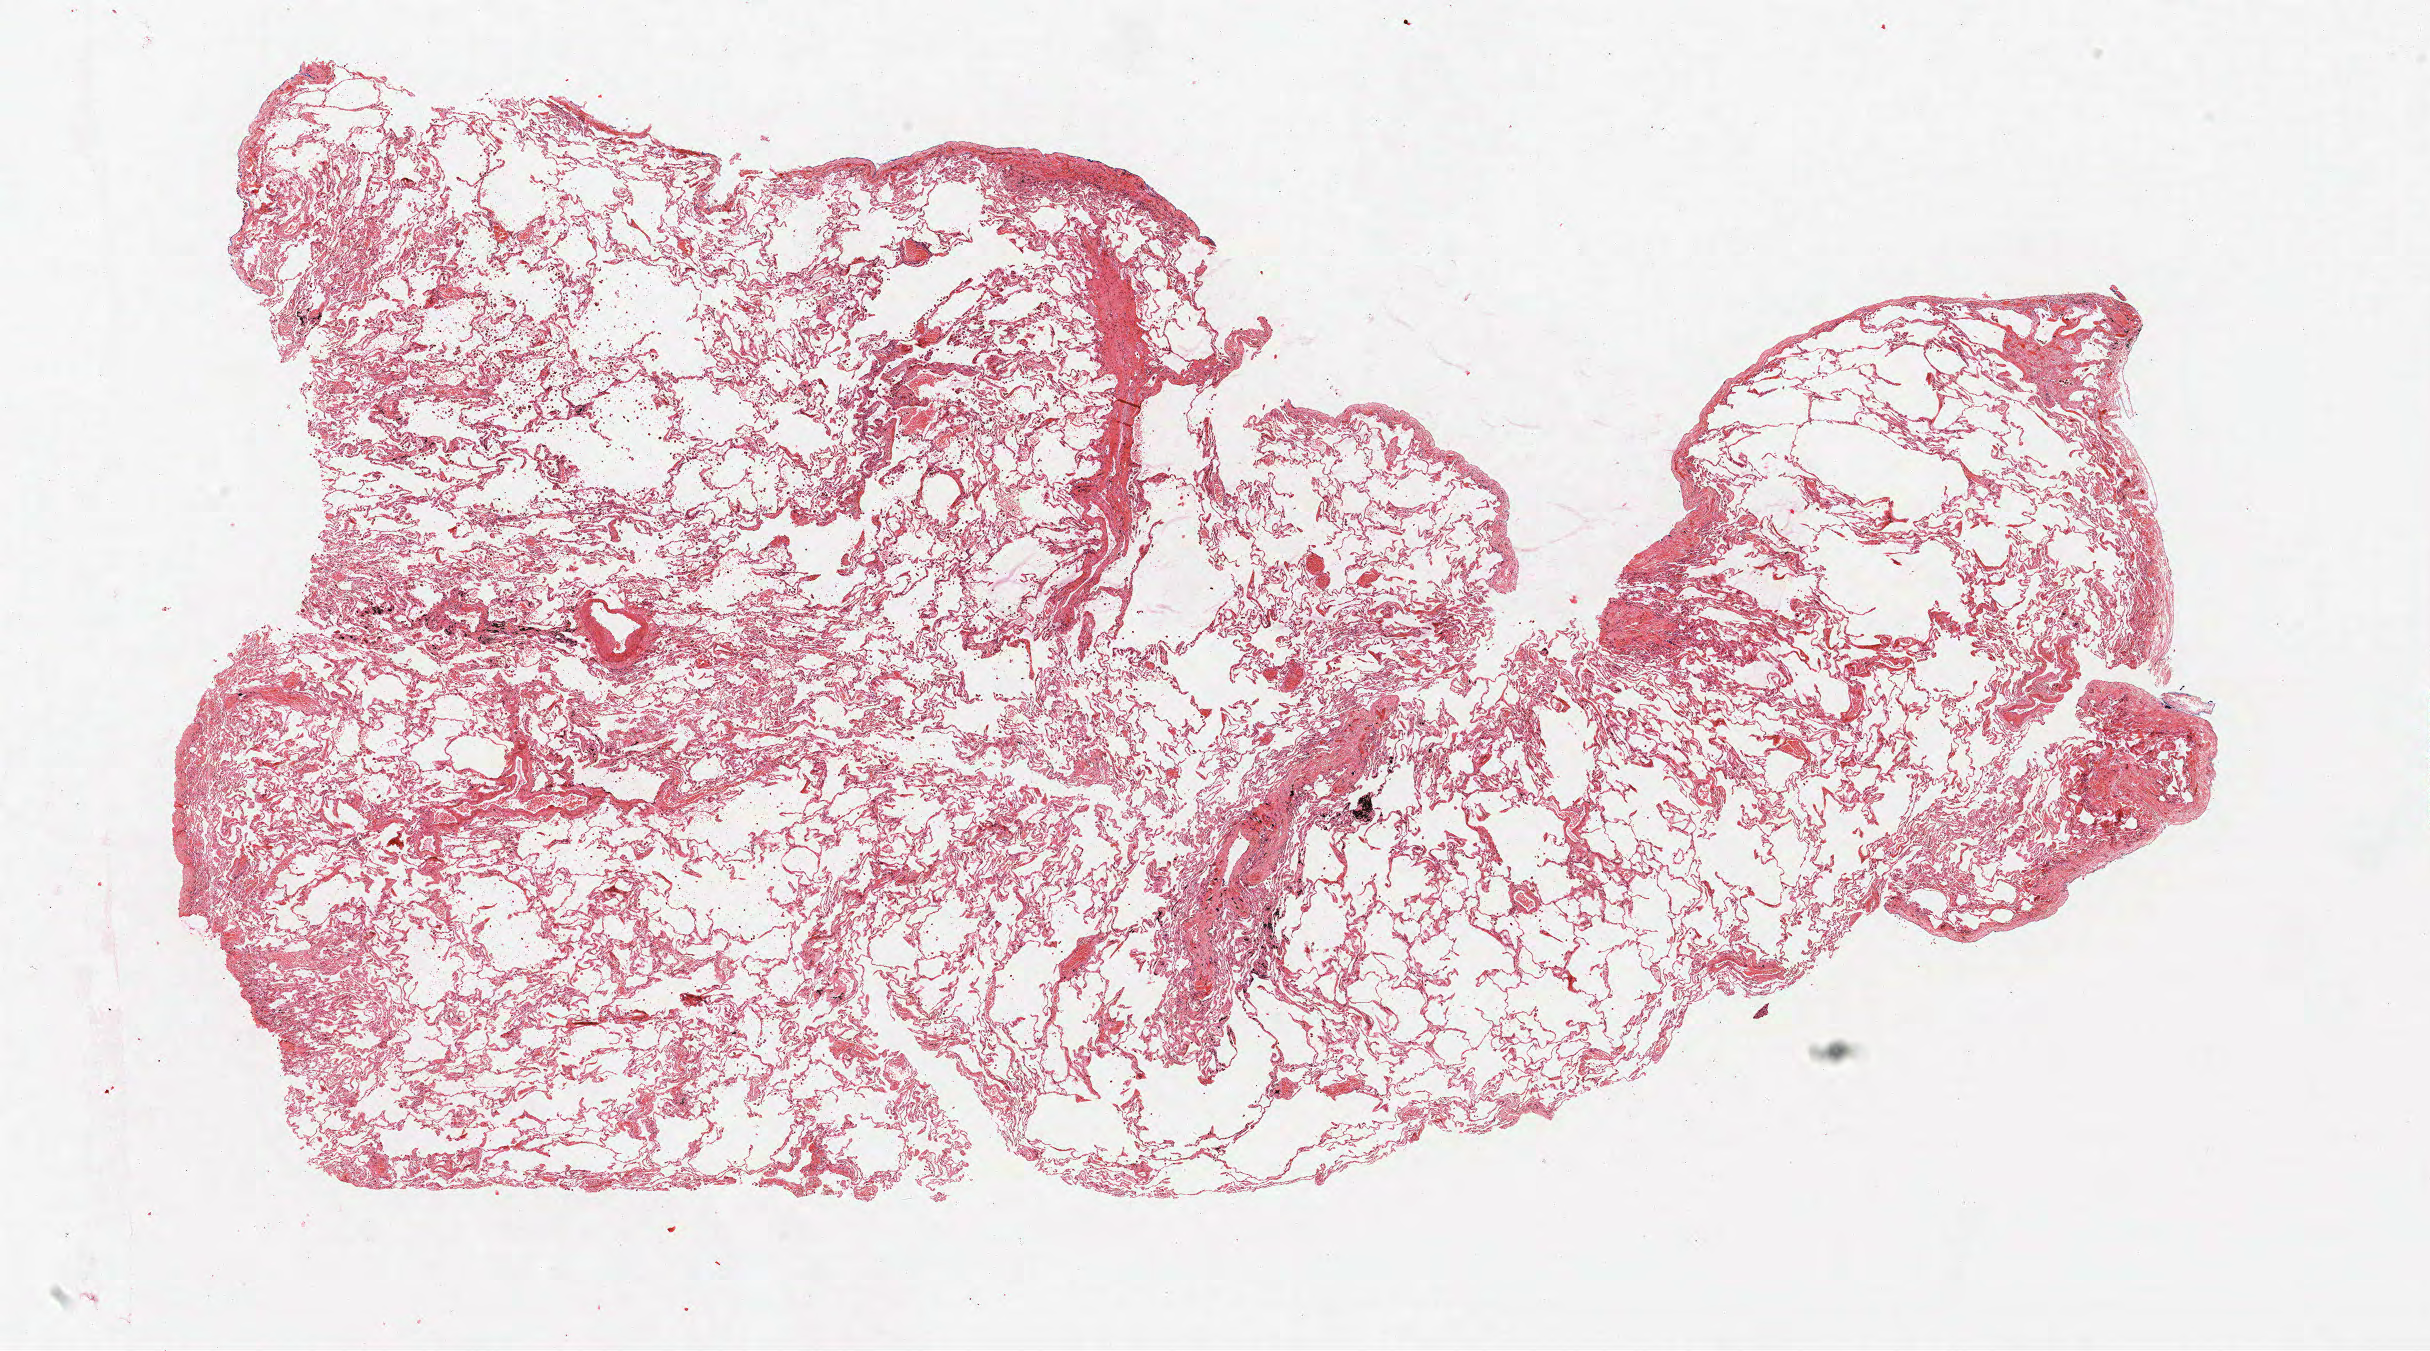
Whole-slide histology image, H&E, low-resolution overview of the scanned area, about 19.4 x 10.8 mm (acquisition: 40x scan), formalin-fixed paraffin-embedded (FFPE) section, lung tissue. Female patient, aged 63 at enrolment. Grade: moderately differentiated (G2).
ICD-O-3 topography: lower lobe of lung (C34.3). Stage (AJCC 6th edition): IB. Participant's lung-cancer diagnosis: Squamous cell carcinoma, NOS (ICD-O-3 8070/3). Primary tumour location (clinical record): left lower lobe. Tumour size (pathology): 15 mm.